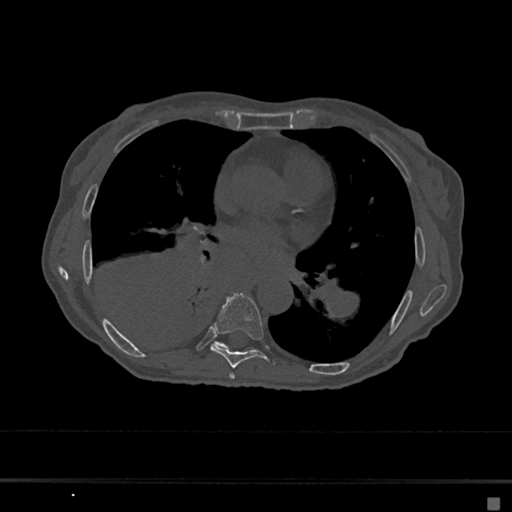
CT including the spine, one axial slice; position 363 of 797 along the scan axis; reconstruction kernel Br40s/3; bone window (W 1800 / L 400 HU); 0.5 mm slice thickness; 512 × 512 image matrix, field of view 360 × 360 mm. Female patient, age 68 years. Case-level facts recorded for this patient, not image findings: primary cancer: renal.
Structures marked on this image (semi-automatically segmented with operator editing):
- T6 vertebra: bounding box <229,373,235,379> (left, top, right, bottom; pixels)
- T7 vertebra: <210,292,273,368>
- T8 vertebra: <216,342,228,348>